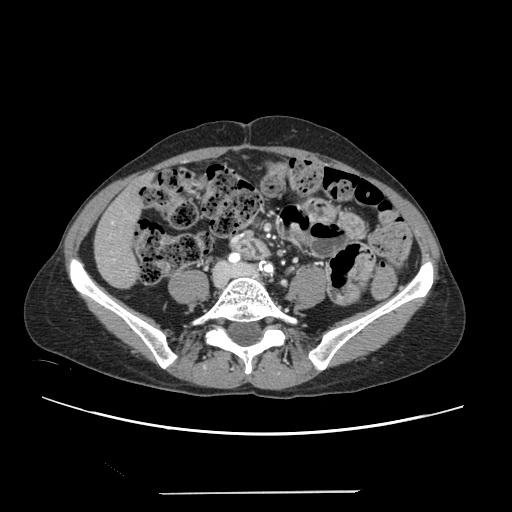
Contrast-enhanced abdominal CT, one axial slice; slice 30 of 240 in the series (ordered by position); 120 kVp; intravenous contrast given; soft-tissue window (W 400 / L 40 HU); 1.25 mm slice thickness; 512 × 512 image matrix, field of view 371 × 371 mm. Female patient, age 60 years. From the clinical record (not read from this slice): diagnosis: colorectal cancer liver metastases, imaged before liver resection; multiple liver metastases: no; largest metastasis: 1.5 cm; disease in both lobes: no.
Annotated regions visible in this slice (manually delineated by an expert):
- liver: bounding box <95,180,144,287> (left, top, right, bottom; pixels)
- planned liver remnant (the part of the liver to remain after resection): <95,179,145,287>
- portal vein (with intrahepatic branches): <110,221,116,260>